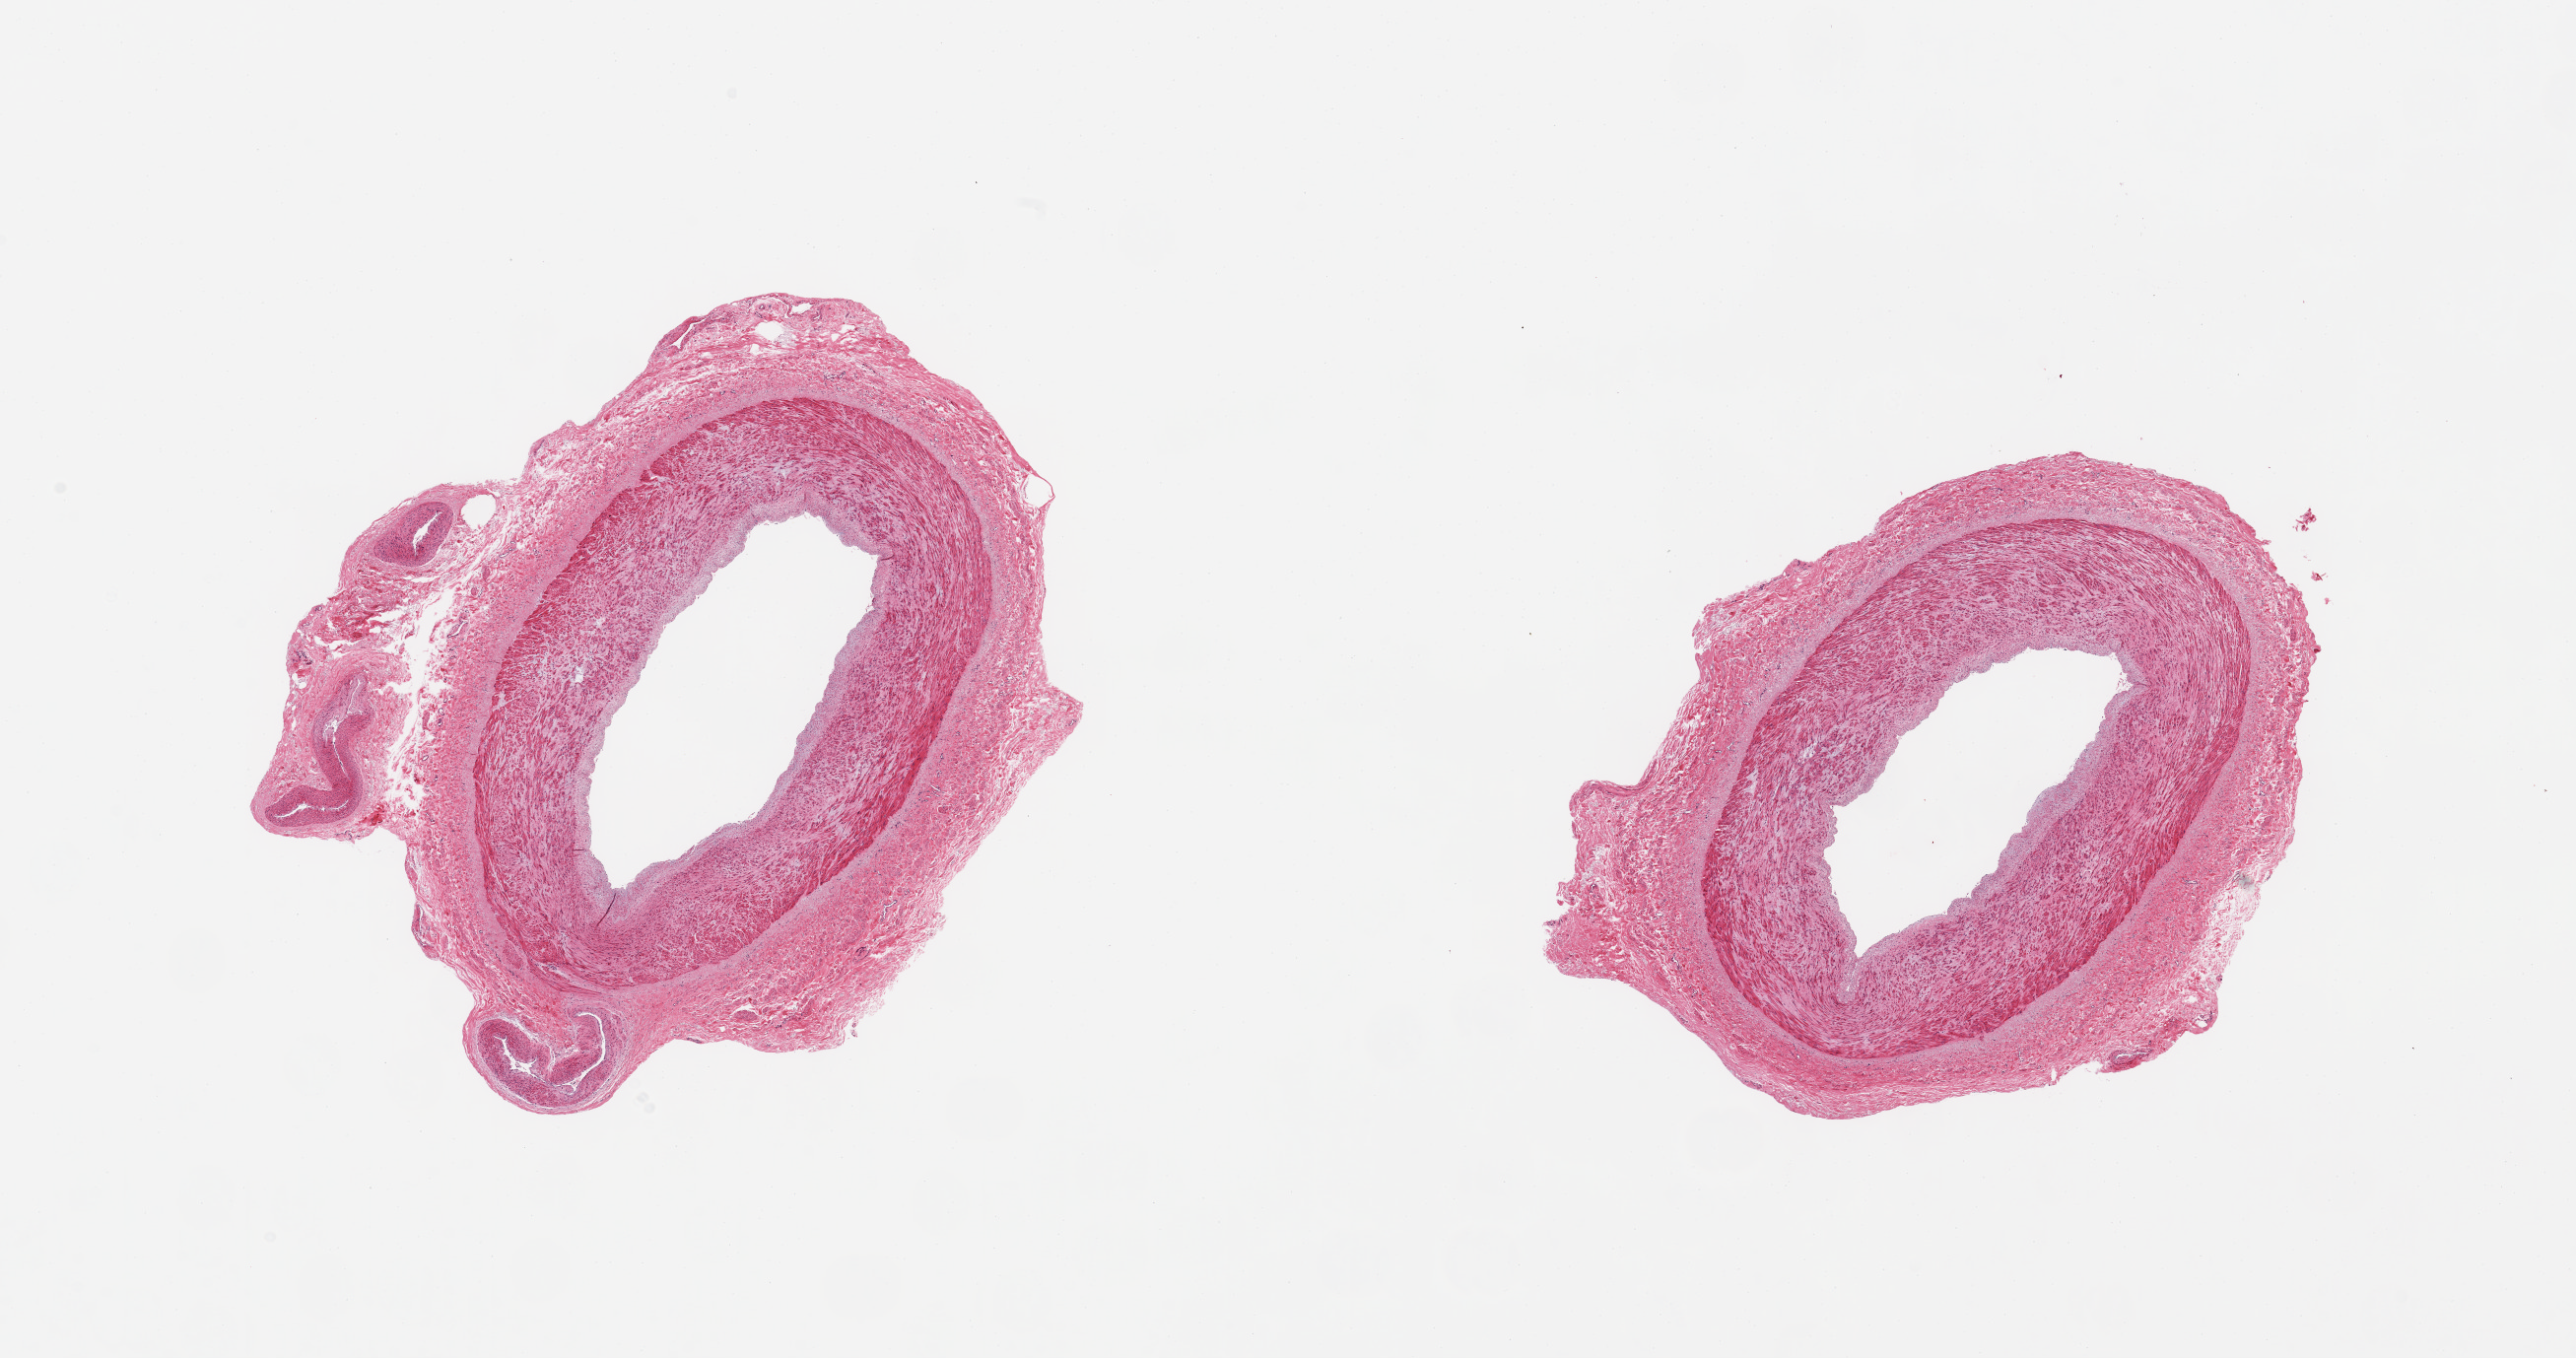
H&E whole-slide image — whole scanned area (about 20.7 x 10.9 mm) shown as a low-resolution overview, PAXgene-fixed, paraffin-embedded tissue, target tissue: tibial artery, donor tissue sample. Donor sex: male.
Review note (as recorded): 2 pieces; intimal thickening.